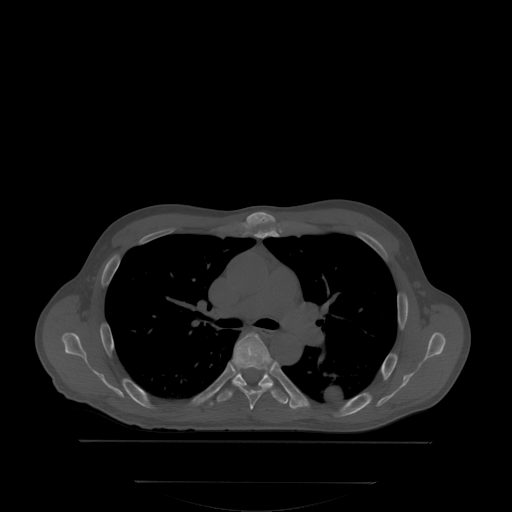
CT including the spine, one axial slice. Position 243 of 350 along the scan axis. Bone window (W 1800 / L 400 HU). 2.5 mm slice thickness. 512 × 512 image matrix. Male patient, age 58 years. From the clinical record (not read from this slice): primary cancer: prostate; vertebrae with lytic lesions (as recorded): L1.
Outlined on this slice (semi-automatic segmentation, software-assisted and operator-edited):
- T5 vertebra: box from (x=233, y=334) to (x=272, y=409) px
- T6 vertebra: (x=210, y=371)–(x=302, y=405)